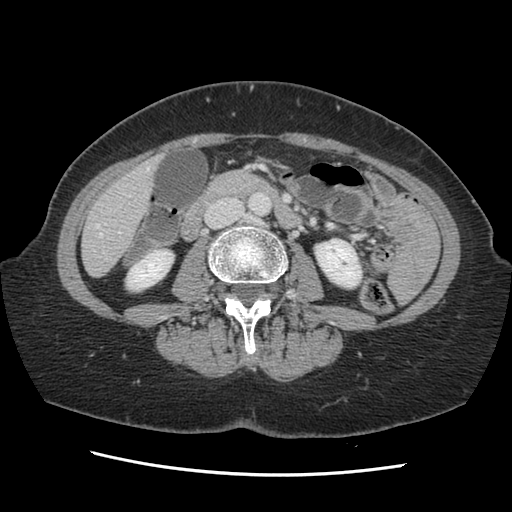
Contrast-enhanced abdominal CT, one axial slice; slice 39 of 141 in the series (ordered by position); 120 kVp; soft-tissue window (W 400 / L 40 HU); 2.5 mm slice thickness; 512 × 512 image matrix. Female patient, age 61 years. Case-level facts recorded for this patient, not image findings: diagnosis: colorectal cancer liver metastases, imaged before liver resection; multiple liver metastases: no; largest metastasis: 2.4 cm; chemotherapy before resection: no.
Structures marked on this image (expert manual segmentation):
- hepatic veins: bounding box [x1, y1, x2, y2] px = [97, 163, 150, 237]
- liver: [83, 159, 159, 276]
- planned liver remnant (the part of the liver to remain after resection): [83, 166, 156, 276]